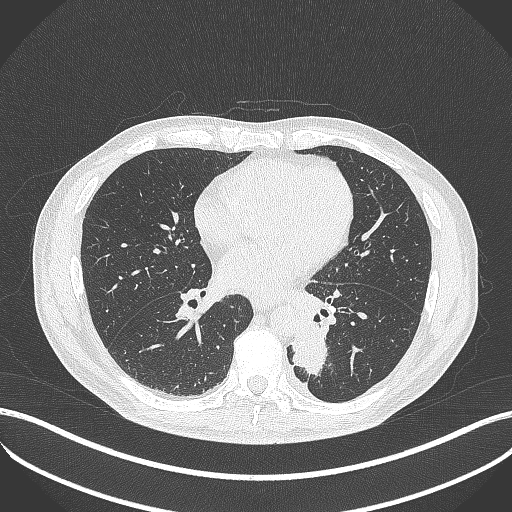
Chest CT, one axial slice. Position 179 of 451 along the scan axis. Reconstruction kernel B70f. Lung window (W 1500 / L -600 HU). 1 mm slice thickness. 512 × 512 image matrix, field of view 400 × 400 mm. Patient: male, 72 years. Case-level facts recorded for this patient, not image findings: clinical TNM (as recorded): T2b N0 M1.
Structures marked on this image (rectangle marked by the reading radiologist):
- lung tumour (recorded histology: adenocarcinoma): bounding box <289,316,331,382> (left, top, right, bottom; pixels)